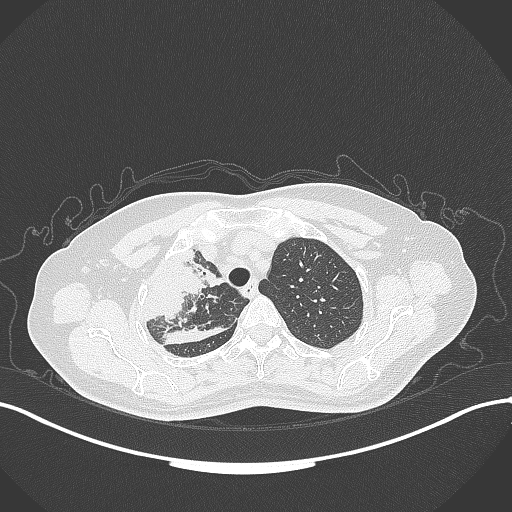
Chest CT, one axial slice; slice 258 of 309 in the series (ordered by position); reconstruction kernel B70f; 120 kVp; lung window (W 1500 / L -600 HU); 1 mm slice thickness; 512 × 512 image matrix. Female patient, age 60 years. From the clinical record (not read from this slice): clinical TNM (as recorded): T3 N1 M1.
Outlined on this slice (bounding box drawn by a radiologist):
- lung tumour (recorded histology: adenocarcinoma): bounding box (x1, y1, x2, y2) in pixels: (131, 237, 224, 321)